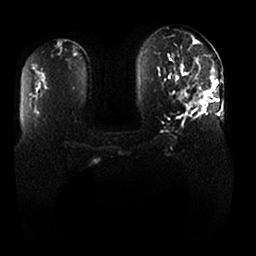
Breast MRI, one axial slice. Position 15 of 25 along the scan axis. Diffusion-weighted series; image 2 of 4 stored at this slice position (different b-values; order by instance number). 1.5 T. 4 mm slice thickness. 256 × 256 image matrix, field of view 370 × 370 mm. Female patient.
Outlined on this slice (expert manual segmentation):
- tumour on diffusion-weighted imaging: bounding box <176,91,210,104> (left, top, right, bottom; pixels)